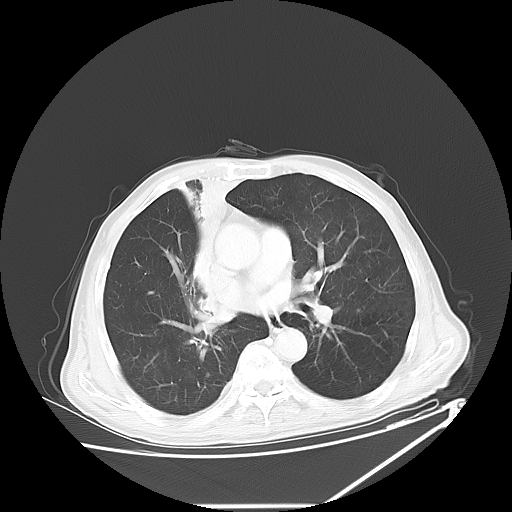
Chest CT, one axial slice. Position 34 of 60 along the scan axis. 120 kVp. Lung window (W 1500 / L -600 HU). 512 × 512 image matrix, field of view 410 × 410 mm. Male patient, age 73 years. Case-level facts recorded for this patient, not image findings: clinical TNM (as recorded): T2a N1 M0.
Outlined on this slice (bounding box drawn by a radiologist):
- lung tumour (recorded histology: squamous cell carcinoma): bounding box [x1, y1, x2, y2] px = [175, 169, 230, 247]